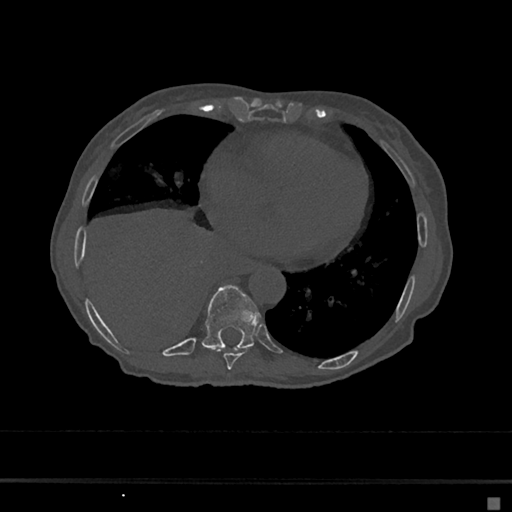
CT including the spine, one axial slice; position 293 of 797 along the scan axis; bone window (W 1800 / L 400 HU); 0.5 mm slice thickness; 512 × 512 image matrix, field of view 360 × 360 mm. Female patient, age 68 years. Case-level facts recorded for this patient, not image findings: primary cancer: renal.
Annotated regions visible in this slice (semi-automatic segmentation, software-assisted and operator-edited):
- T8 vertebra: bounding box (x1, y1, x2, y2) in pixels: (223, 350, 248, 370)
- T9 vertebra: (202, 285, 260, 351)